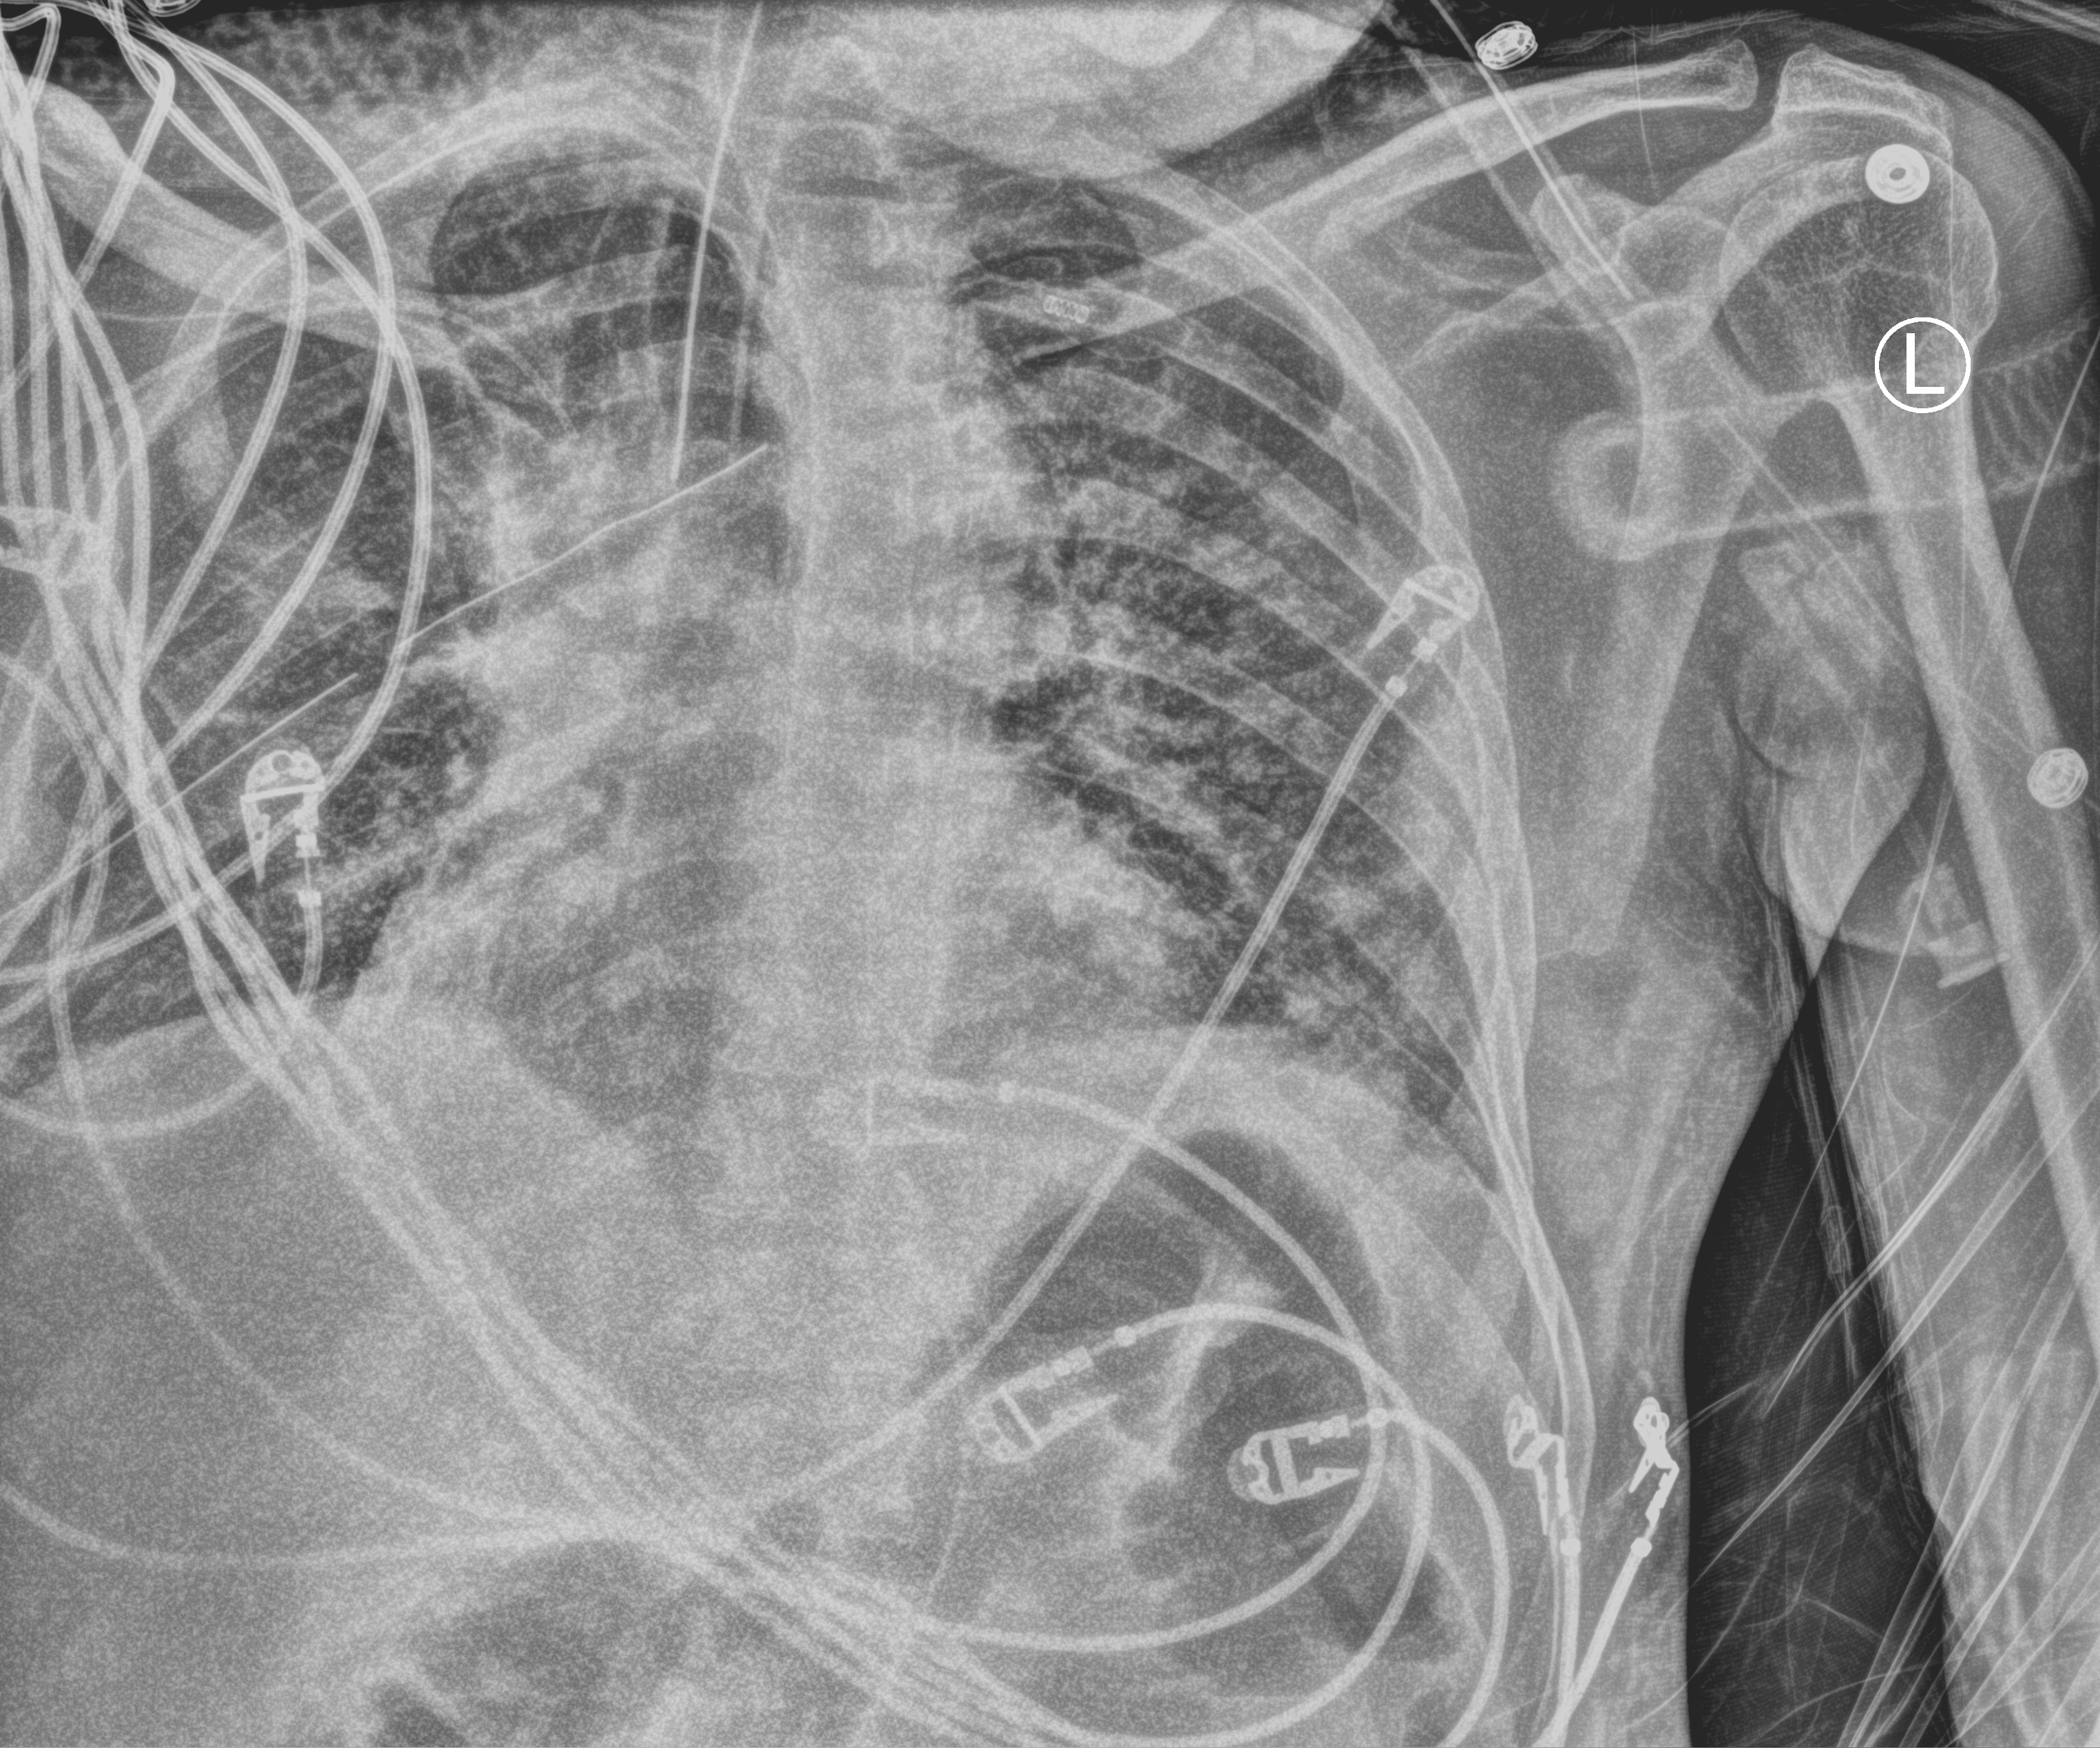
Portable chest radiograph; anteroposterior (AP) projection. Patient hospitalised with COVID-19; male, aged 18–59 years.
Admission-level facts for this patient (not findings on this image; timing relative to this image not recorded):
- admitted to intensive care during this hospital stay: yes